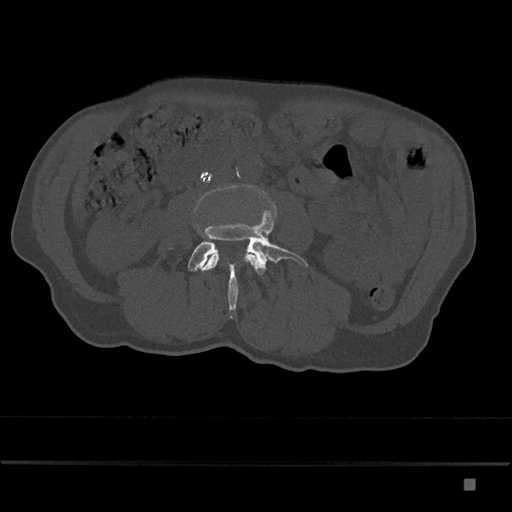
CT including the spine, one axial slice. Position 361 of 797 along the scan axis. Bone window (W 1800 / L 400 HU). 0.5 mm slice thickness. 512 × 512 image matrix, field of view 390 × 390 mm. Patient: male, 72 years. Case-level facts recorded for this patient, not image findings: primary cancer: prostate.
Annotated regions visible in this slice (semi-automatic segmentation, software-assisted and operator-edited):
- L3 vertebra: box from (x=202, y=253) to (x=259, y=271) px
- L4 vertebra: (x=187, y=210)–(x=308, y=318)